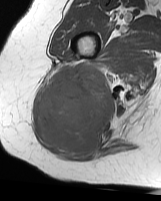
MRI of an extremity soft-tissue mass, one axial slice; slice 37 of 70 in the series (ordered by position); MR volume resampled by the dataset authors to the PET/CT grid (not the native acquisition matrix); 3.27 mm slice thickness; 161 × 201 image matrix, field of view 157 × 196 mm. Female patient. From the clinical record (not read from this slice): histological type: synovial sarcoma; grade: intermediate; site of the primary tumour: right buttock.
Outlined on this slice (expert contour drawn on MRI and transferred to this co-registered scan by the dataset authors):
- gross tumour volume including surrounding oedema: bounding box [x1, y1, x2, y2] px = [37, 61, 114, 157]
- gross tumour volume (mass): [37, 61, 114, 157]